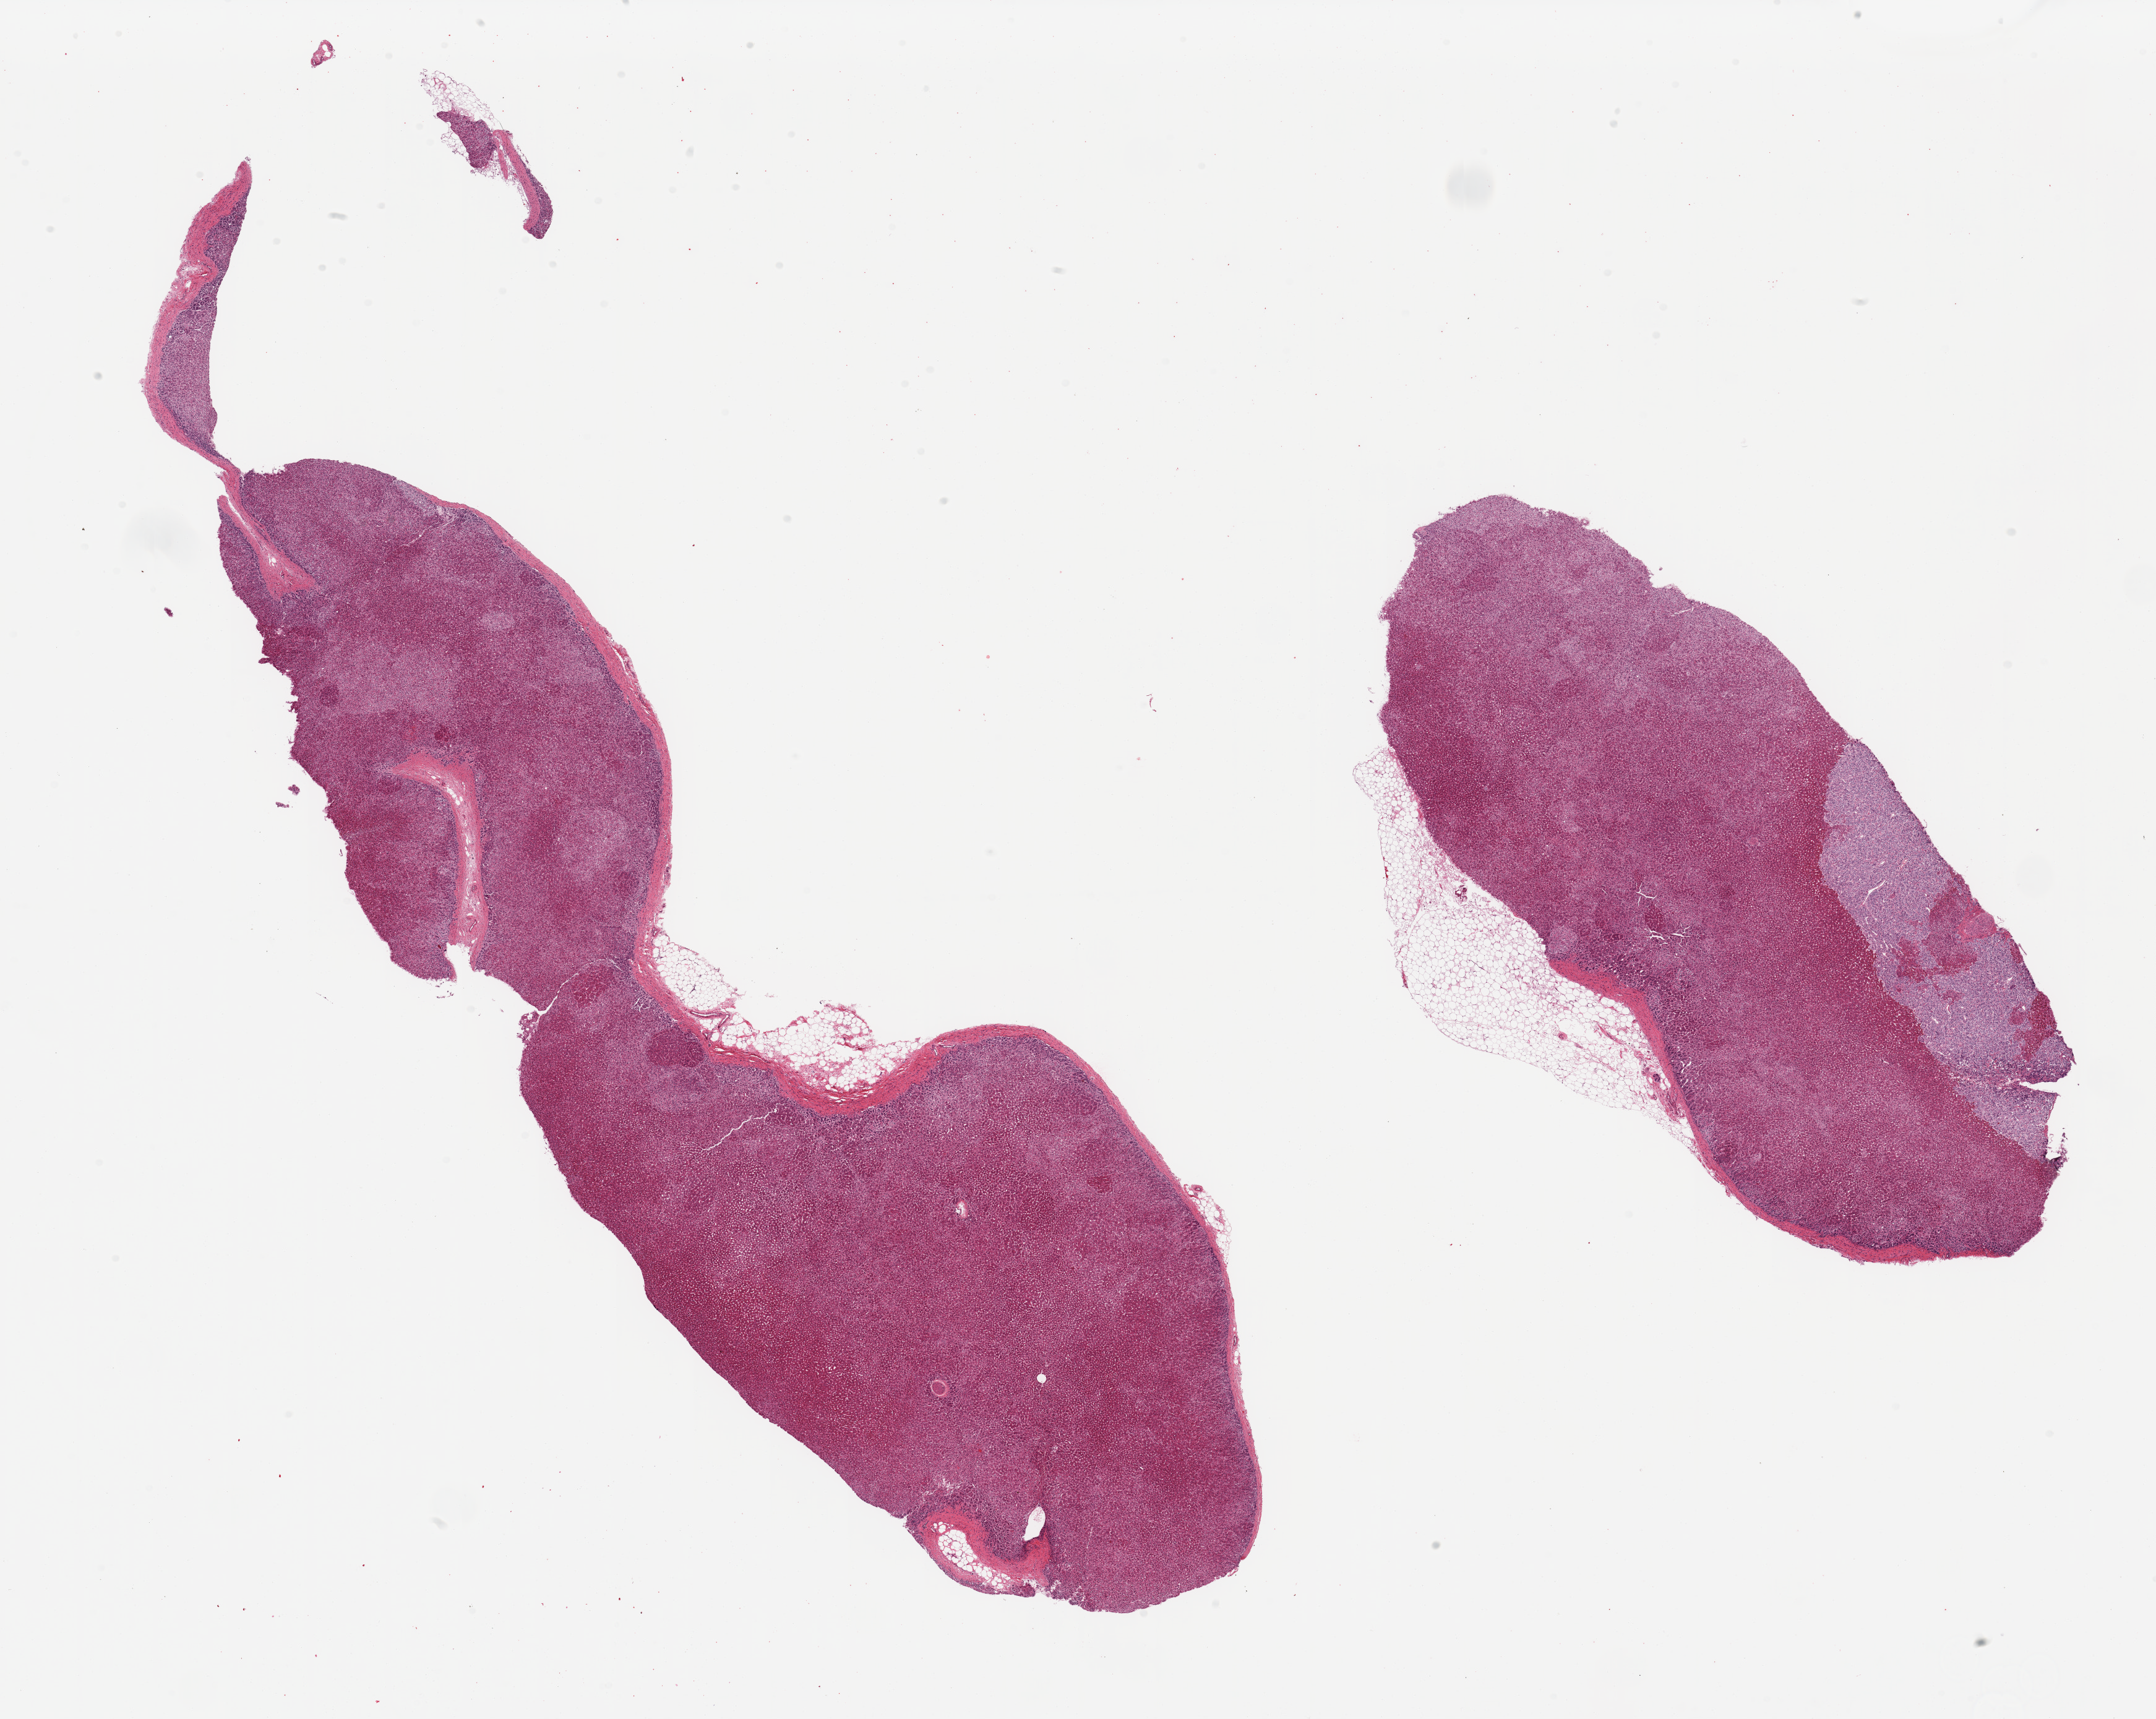
Haematoxylin and eosin whole-slide image — low-resolution overview of the scanned area, about 27.6 x 22.0 mm (slide scanned at 20x). PAXgene-fixed, paraffin-embedded tissue. Target tissue: adrenal gland. Donor tissue sample. Male donor.
Review note (as recorded): 2 pieces, mainly cortex, ~5x1.5mm well preserved focus of medulla (/), valuable specimen; Nubbin of adherent fat, ~1.5mm.